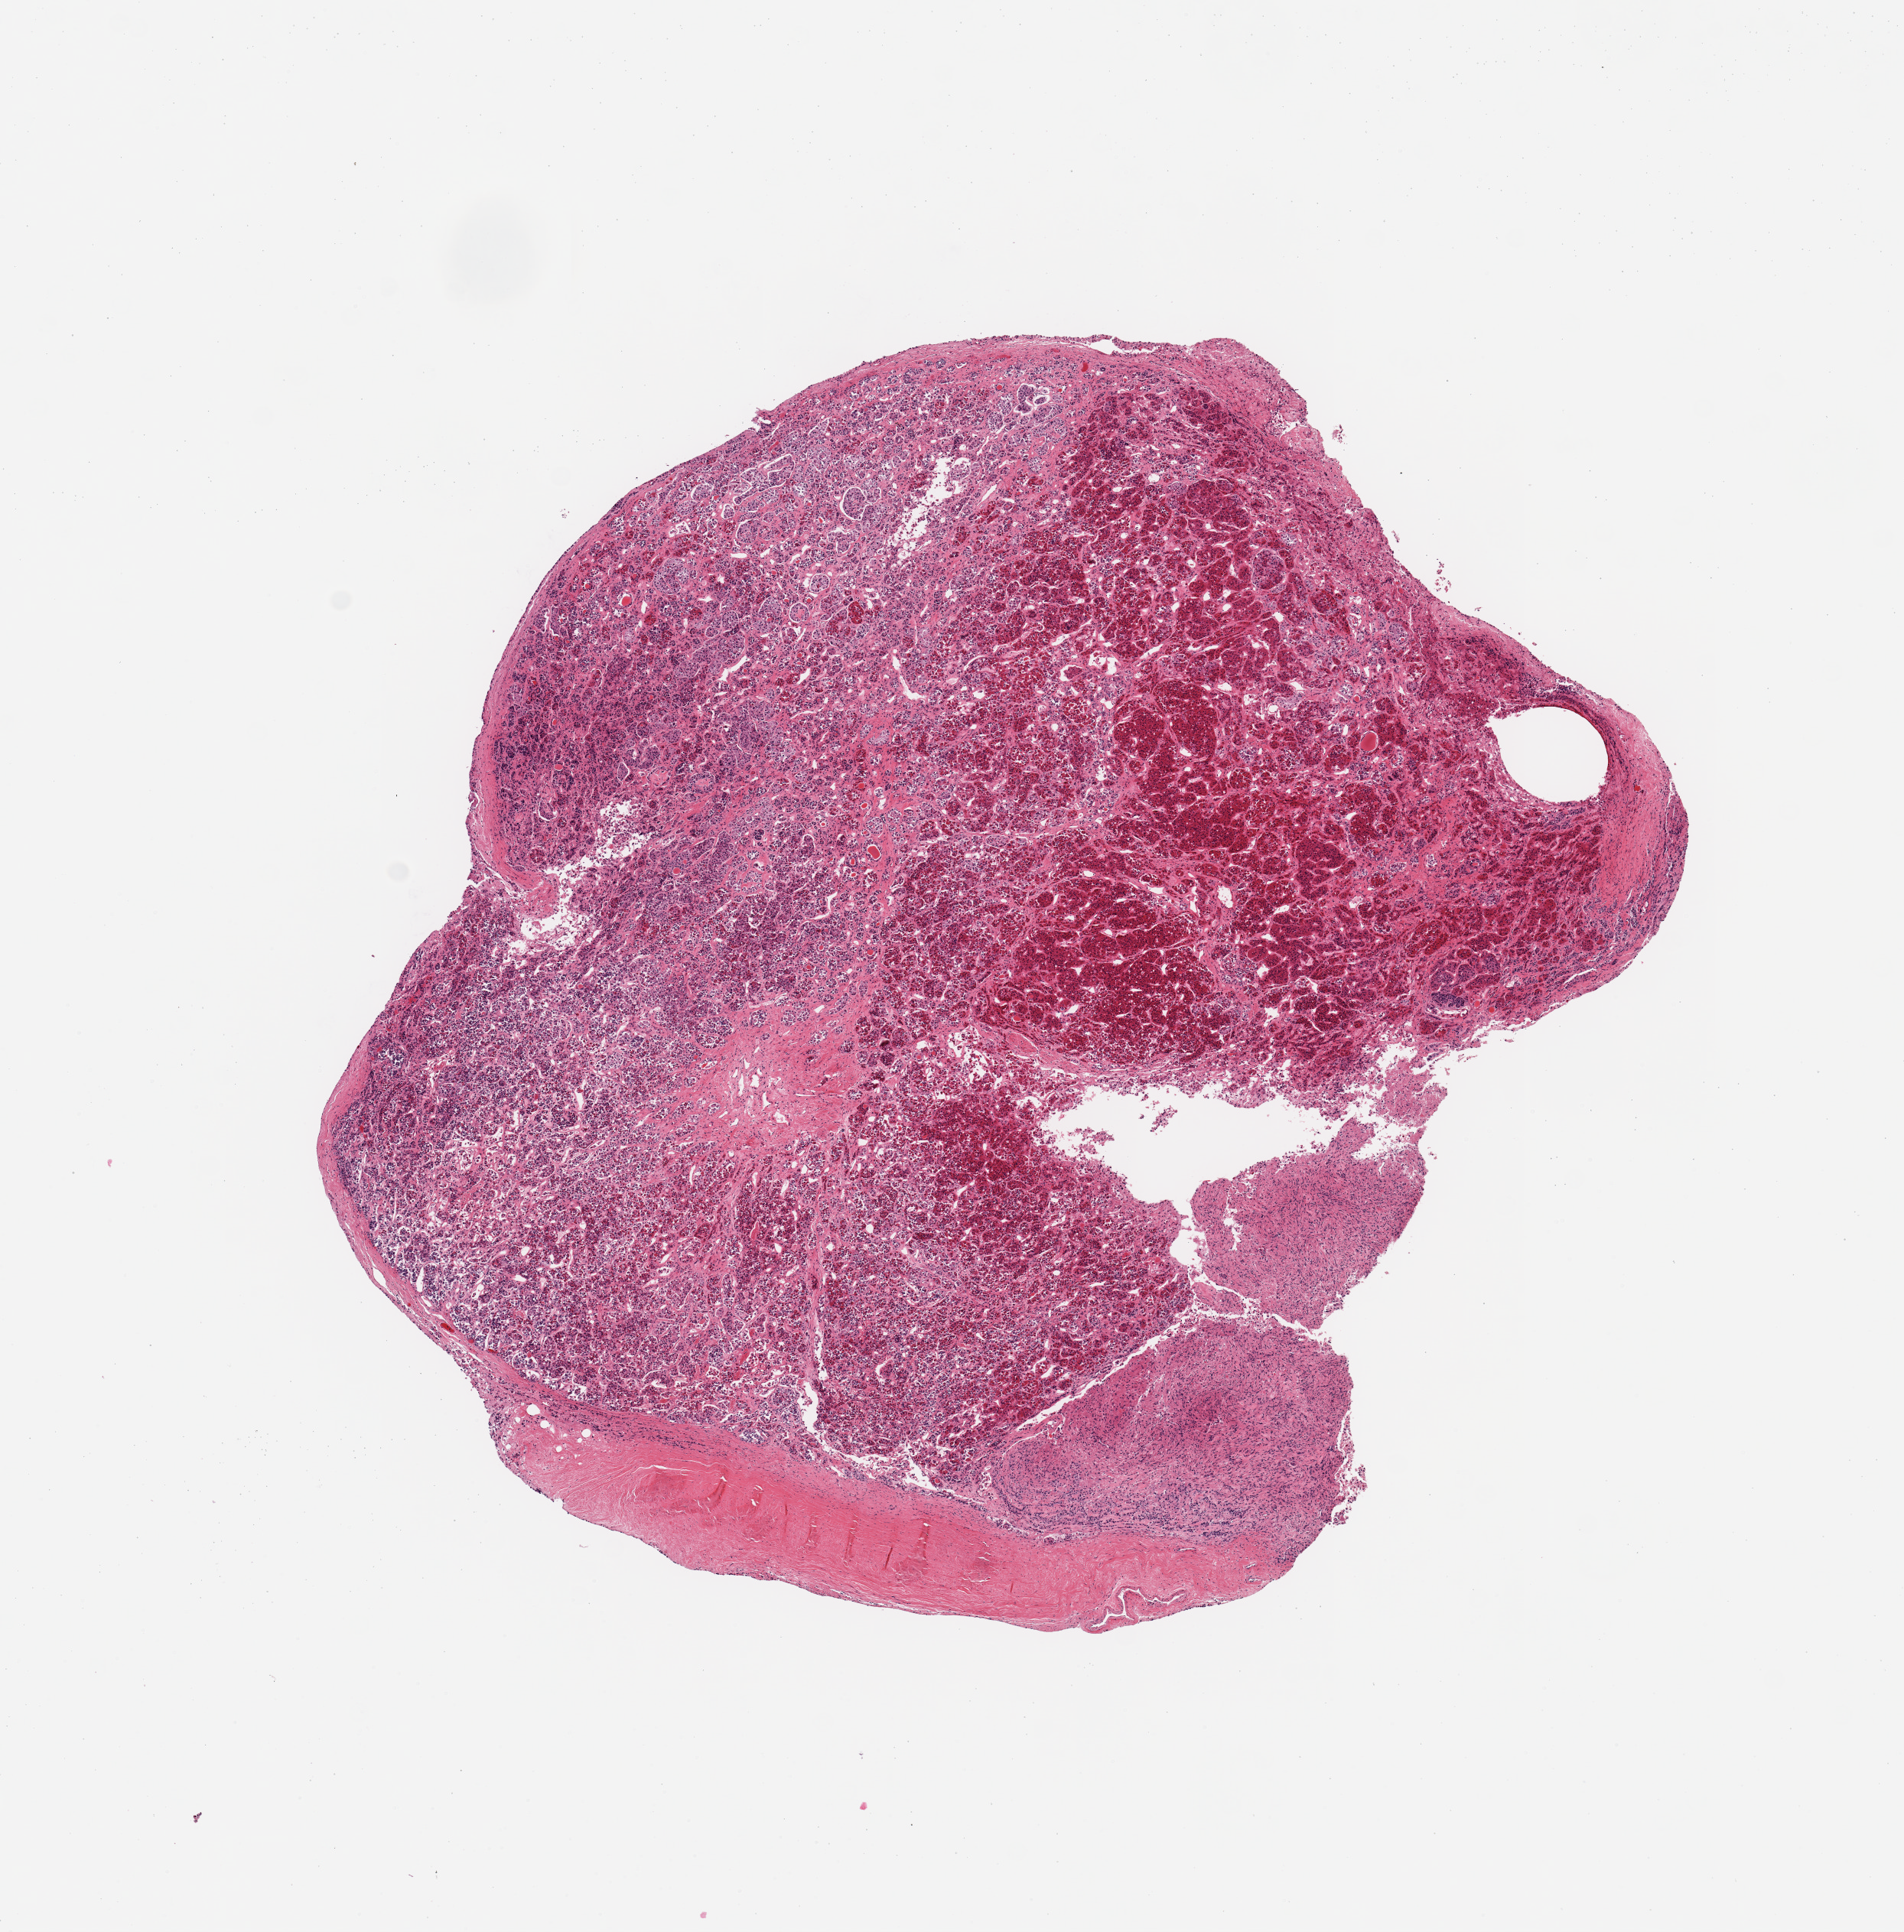
Whole-slide image, haematoxylin and eosin stain, brightfield — a low-resolution overview of the entire scanned area, about 9.8 x 10.0 mm, PAXgene-fixed paraffin-embedded (PFPE) section, section of pituitary (target tissue), tissue donor sample. Donor sex: male.
Pathologist's review note for this sample: 1 piece, mainly adenohypophysis; ~2.5x1mm focus of neurohypophysis.